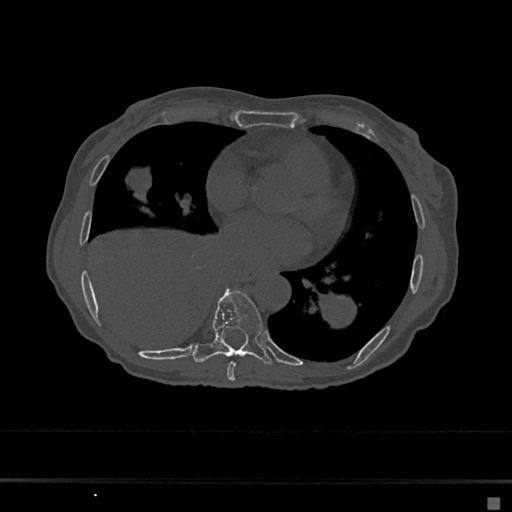
CT including the spine, one axial slice. Slice 332 of 797 in the series (ordered by position). Reconstruction kernel Br40s/3. 120 kVp. Bone window (W 1800 / L 400 HU). 512 × 512 image matrix, field of view 360 × 360 mm. Female patient, age 68 years. Case-level facts recorded for this patient, not image findings: primary cancer: renal.
Outlined on this slice (semi-automatically segmented with operator editing):
- T7 vertebra: bounding box [x1, y1, x2, y2] px = [227, 362, 236, 381]
- T8 vertebra: [192, 290, 272, 365]